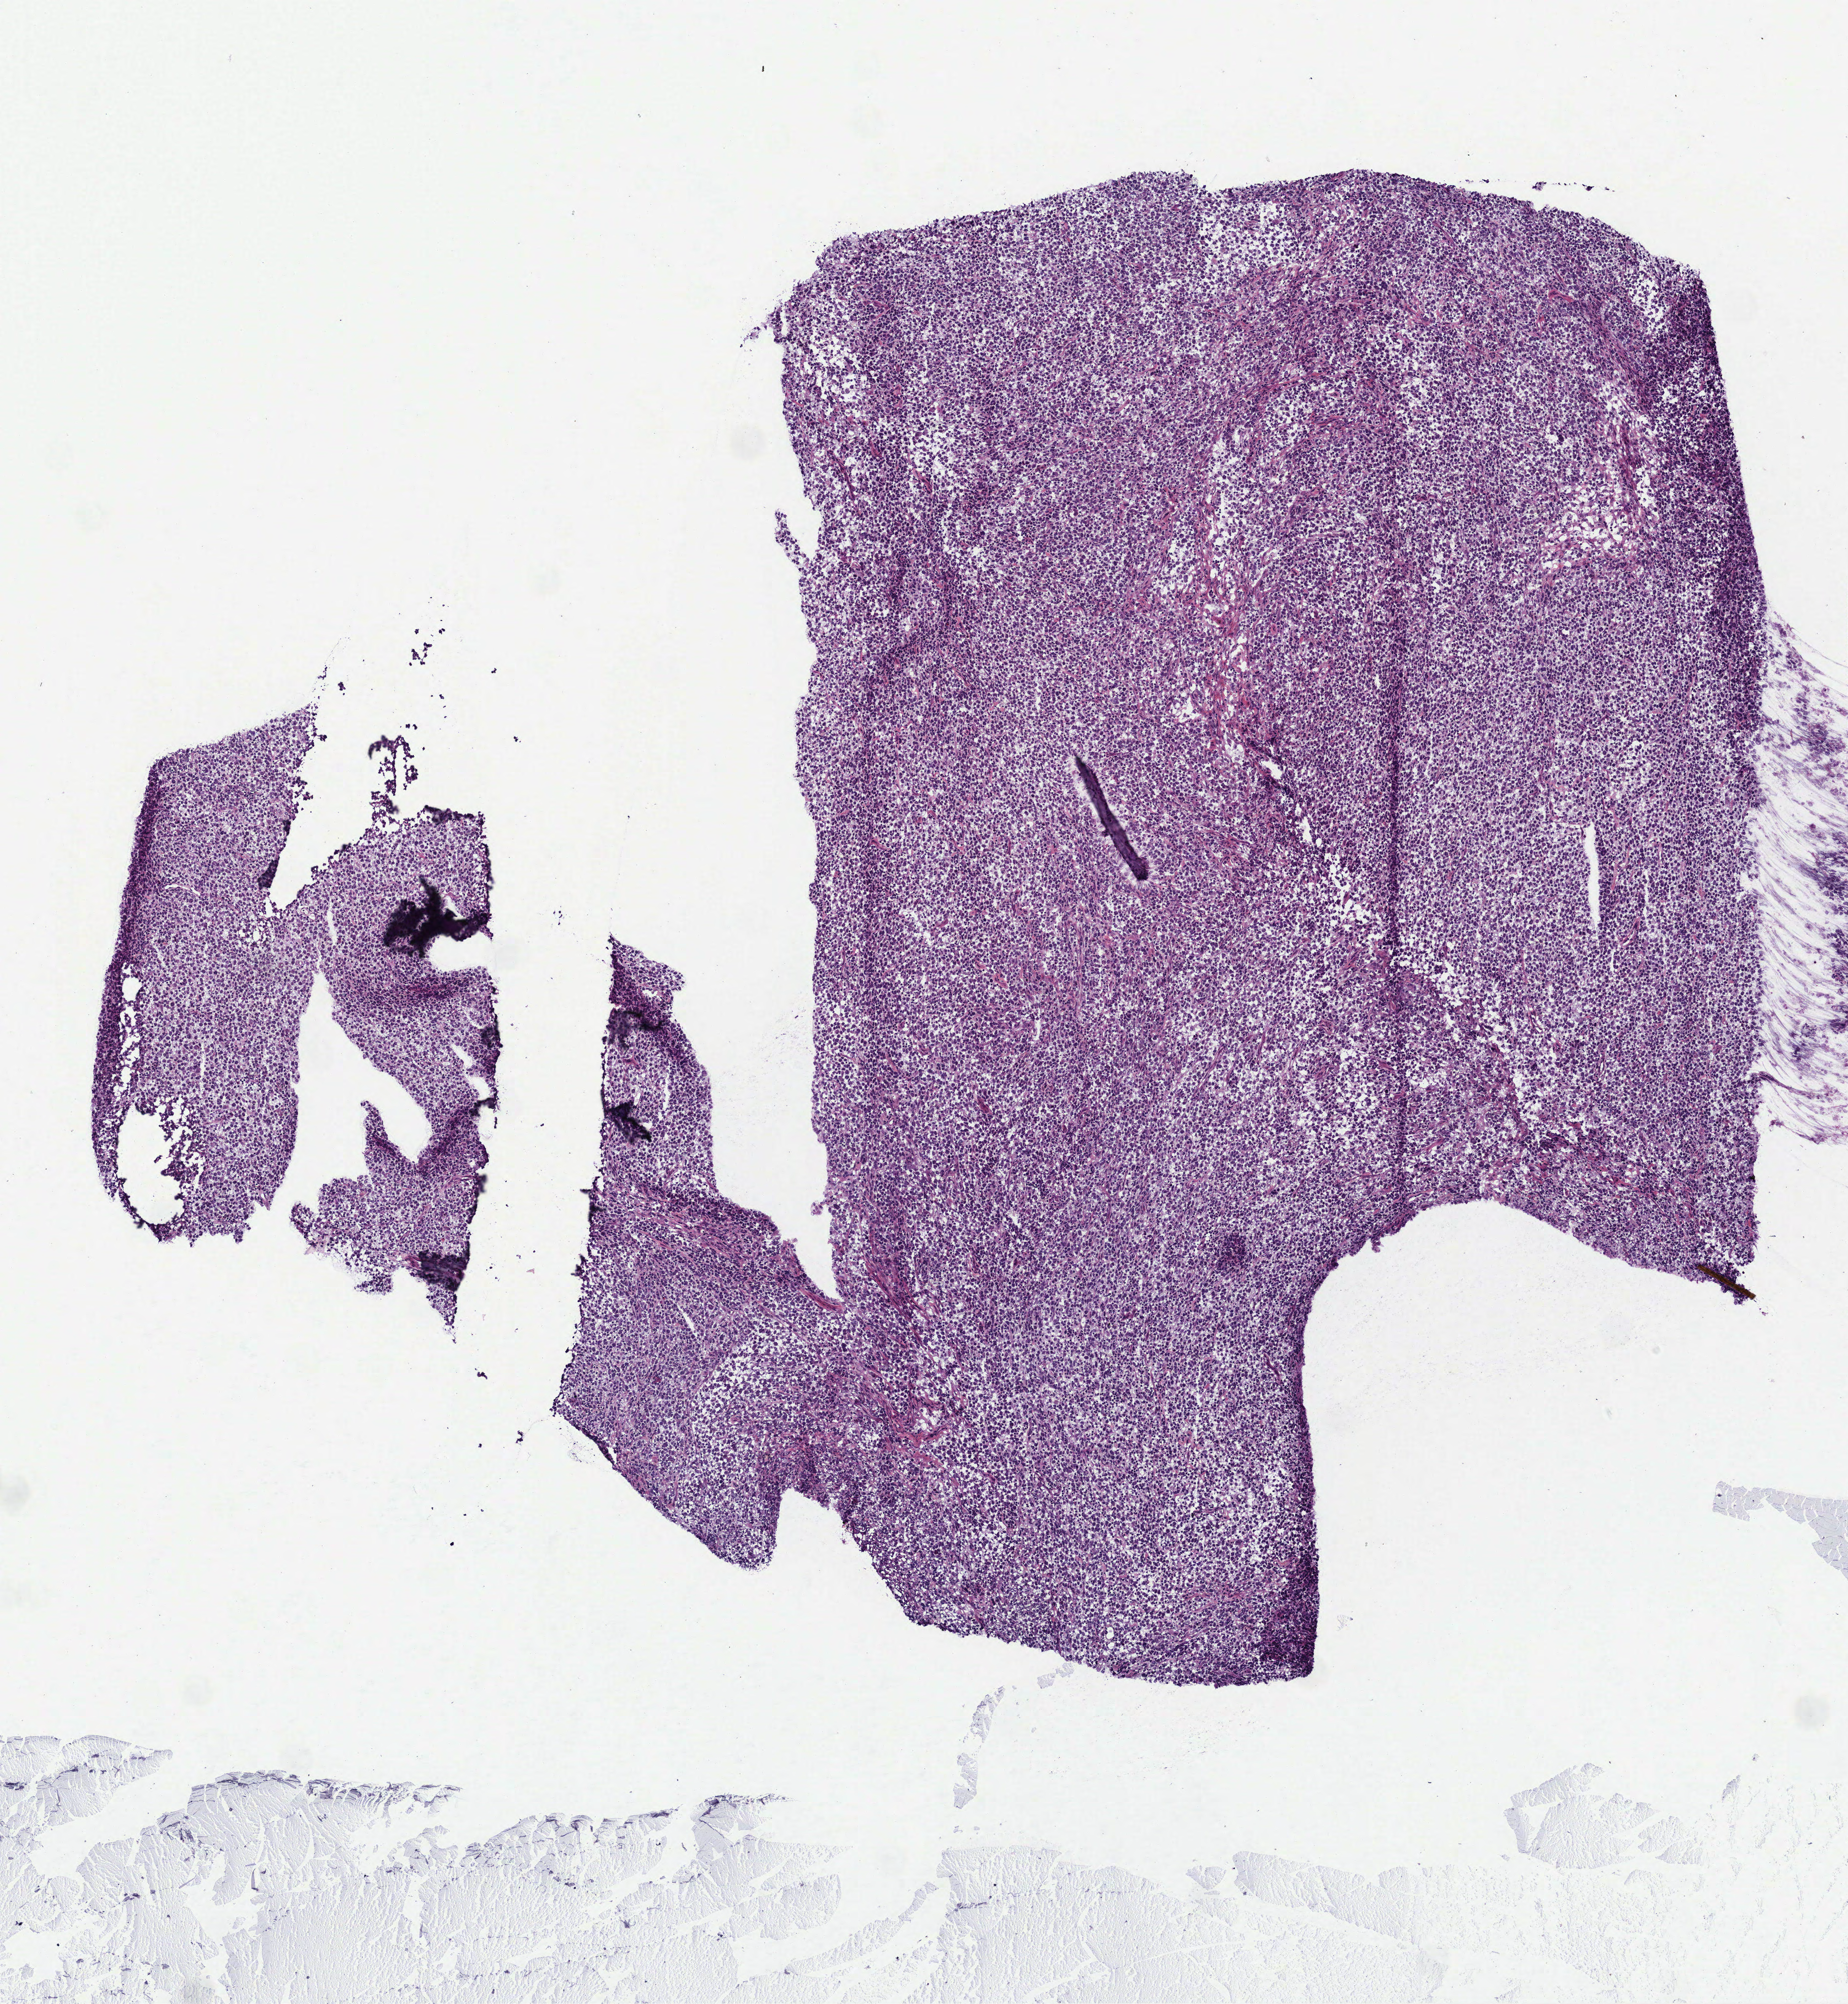
Hematoxylin and eosin (H&E) stained whole-slide image — shown as a low-resolution overview of the whole scanned area (about 5.6 x 6.0 mm, from a 40x scan); frozen section from the top of the tissue portion; lymphoid tissue, primary tumour sample. Patient: female, age at initial diagnosis 28 years. Slide review estimates, as recorded: tumour cells 100%, tumour nuclei 90%, normal cells 0%, stromal cells 0%, necrosis 0%. Inflammatory infiltration, as recorded: lymphocyte infiltration 9%, monocyte infiltration 0%, neutrophil infiltration 0%.
Pathologic diagnosis: Mediastinal (thymic) large B-cell lymphoma (anterior mediastinum).